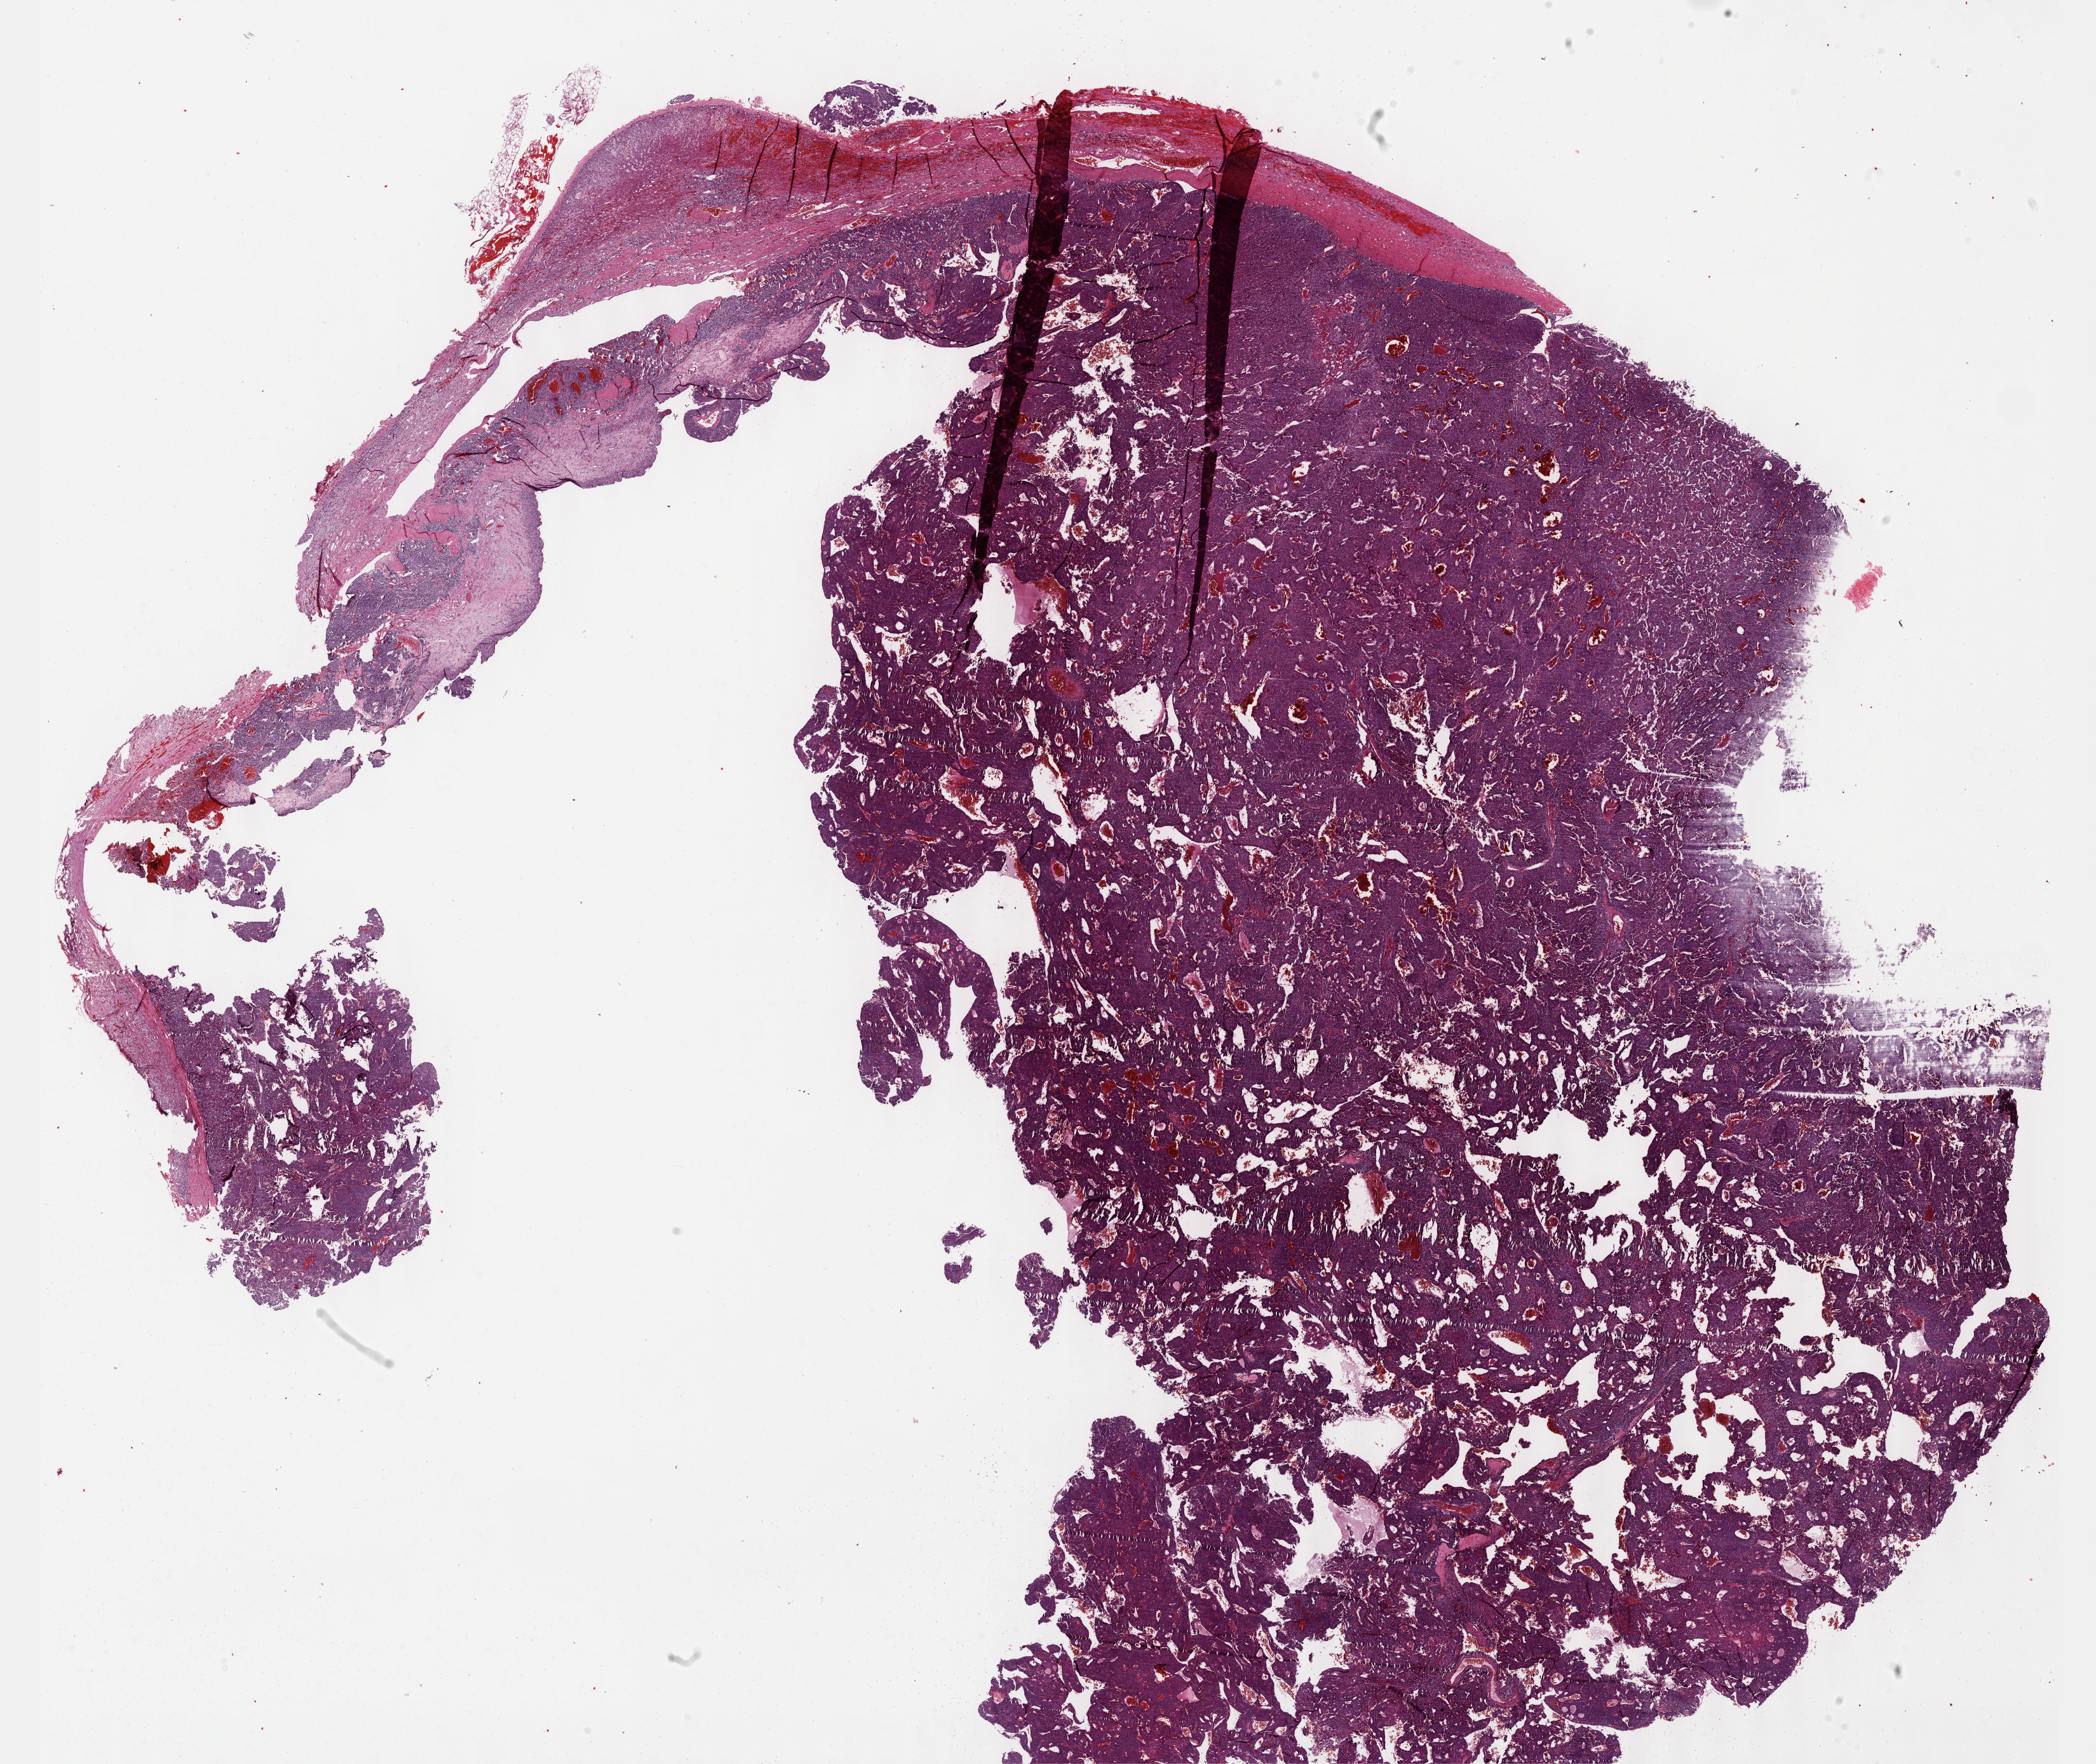
Digitized H&E-stained tissue section (whole slide) — low-resolution overview of the scanned area, about 26.7 x 22.4 mm (acquisition: 40x scan), FFPE section, sample: primary tumour, adrenal gland. Female, age 42 years at initial diagnosis.
Diagnosis: Pheochromocytoma, NOS. Laterality: right.